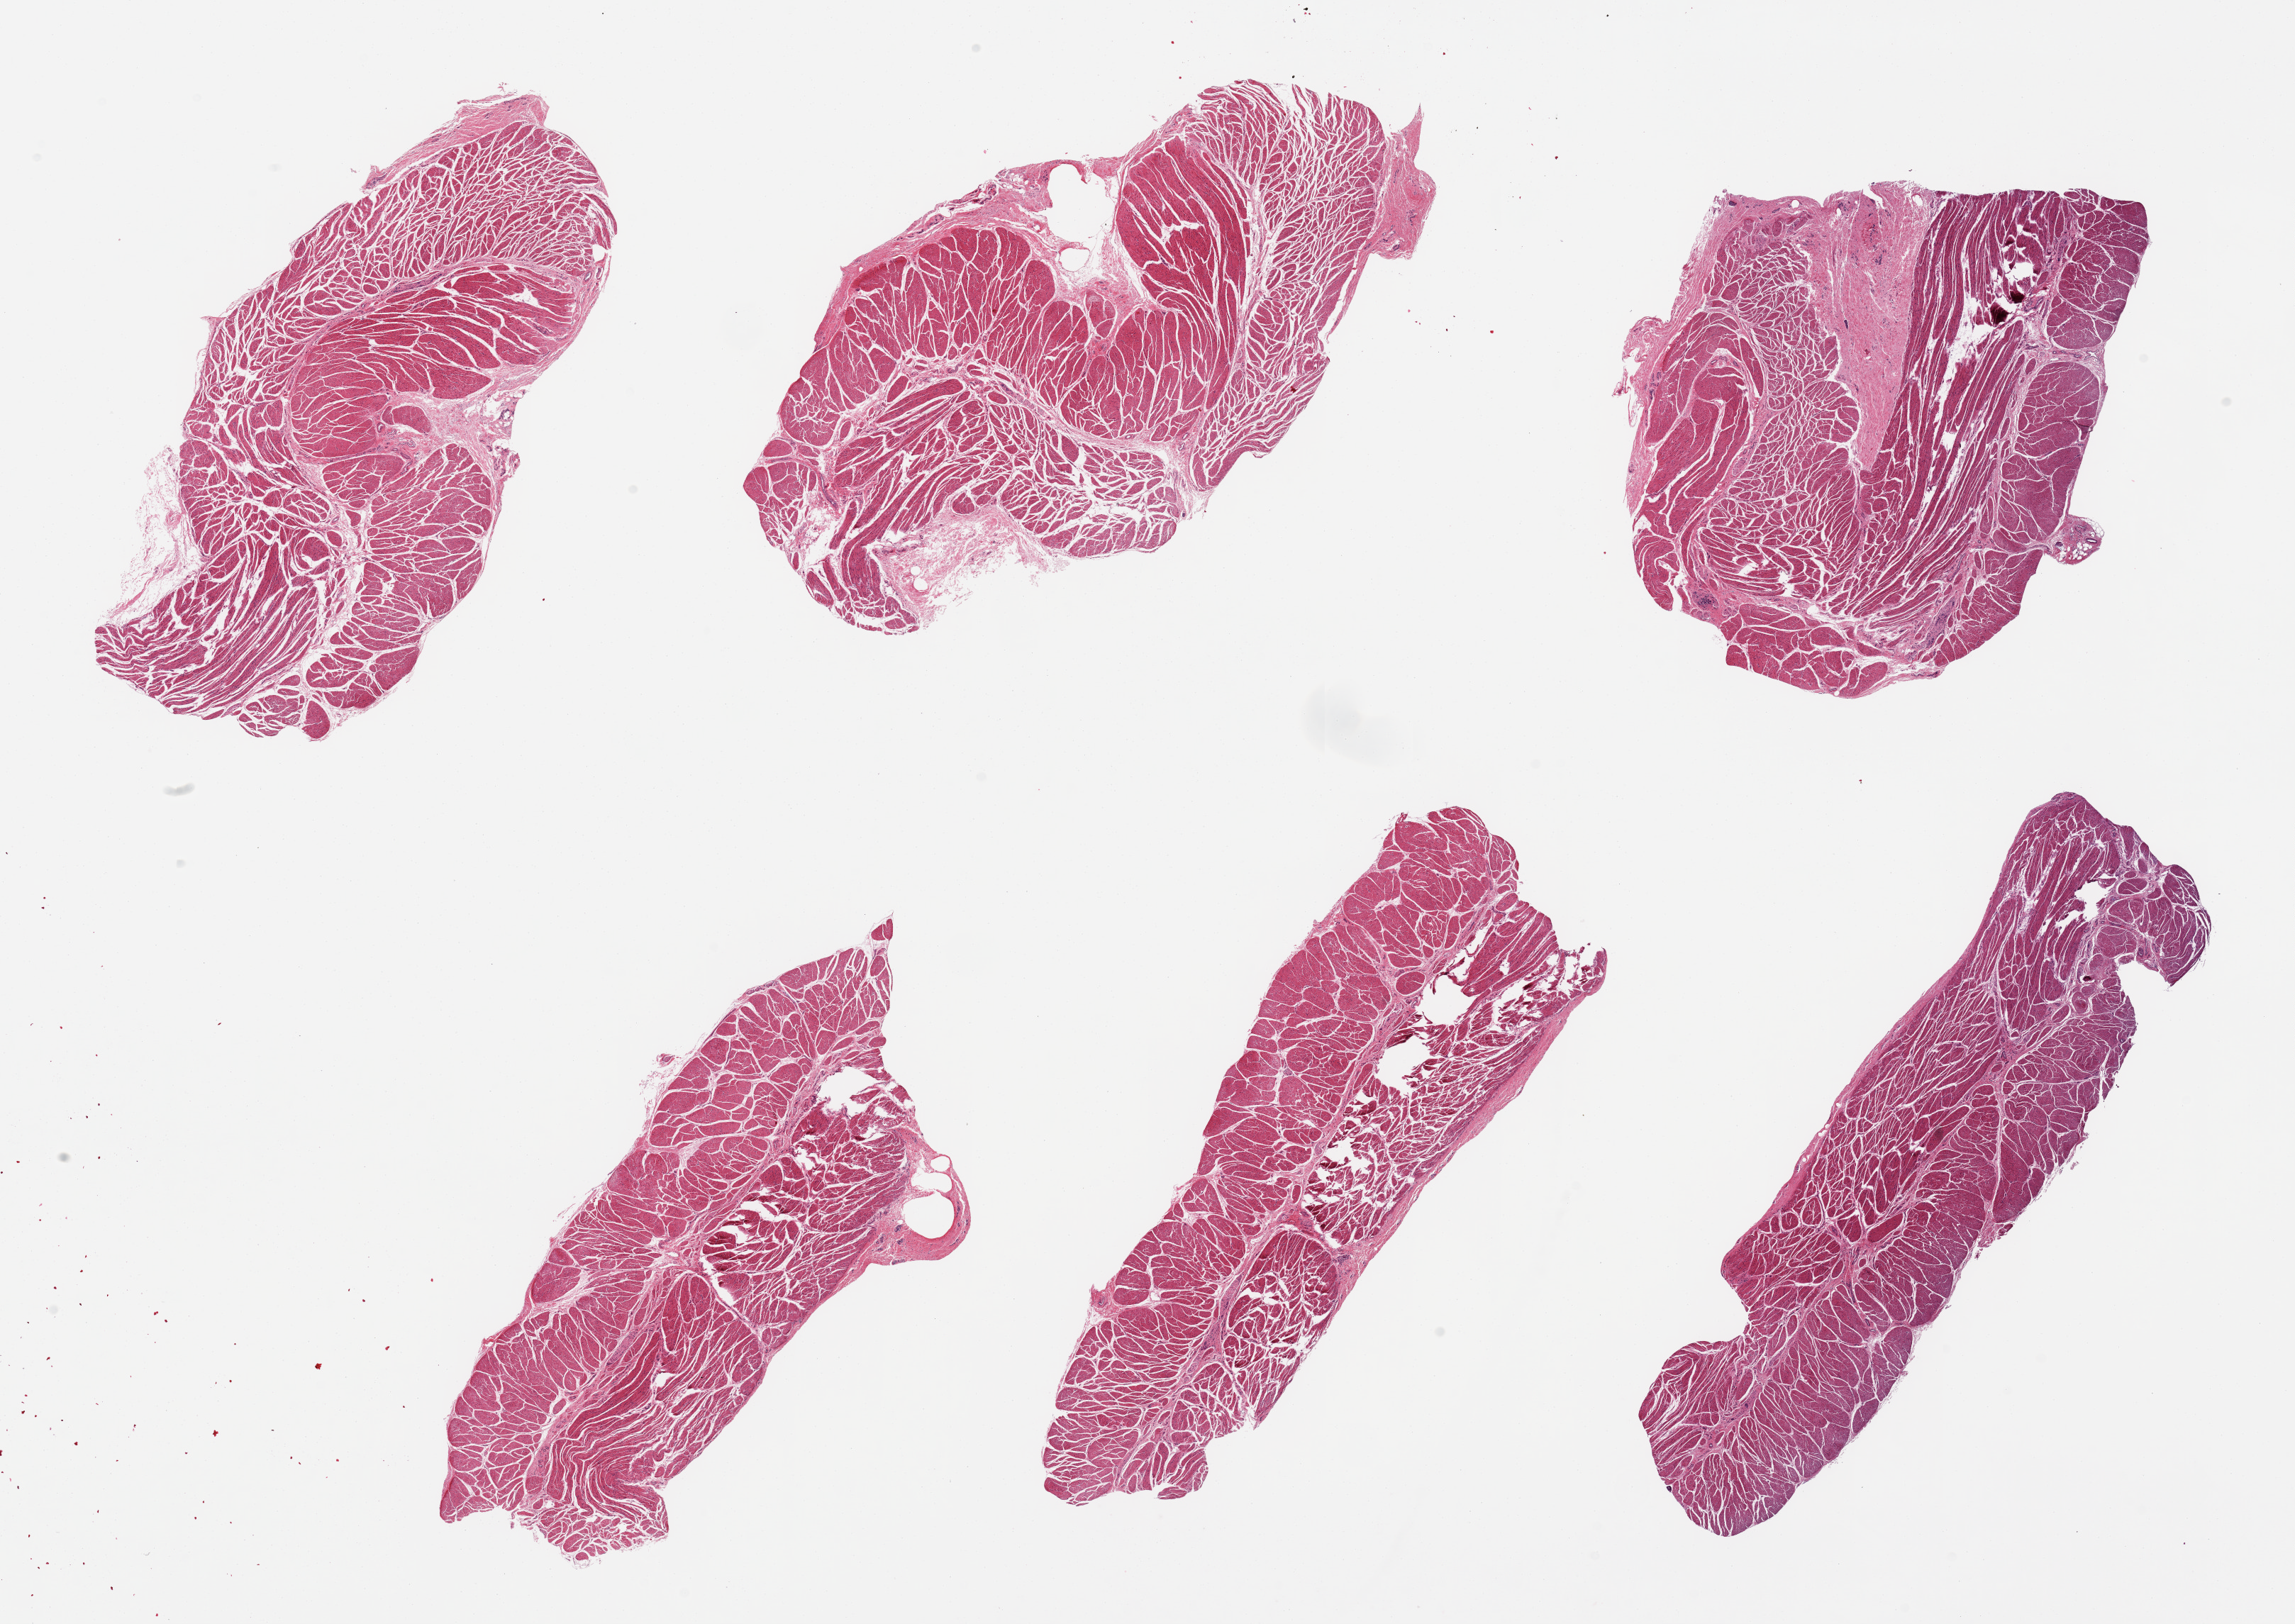
Whole-slide image, H&E stain, a low-resolution overview of the entire scanned area, about 25.6 x 18.1 mm, PAXgene-fixed paraffin-embedded (PFPE) section, section of esophageal muscle (target tissue), tissue donor sample. Donor: male.
* pathologist's review note for this sample: 6 pieces; well dissected muscularis